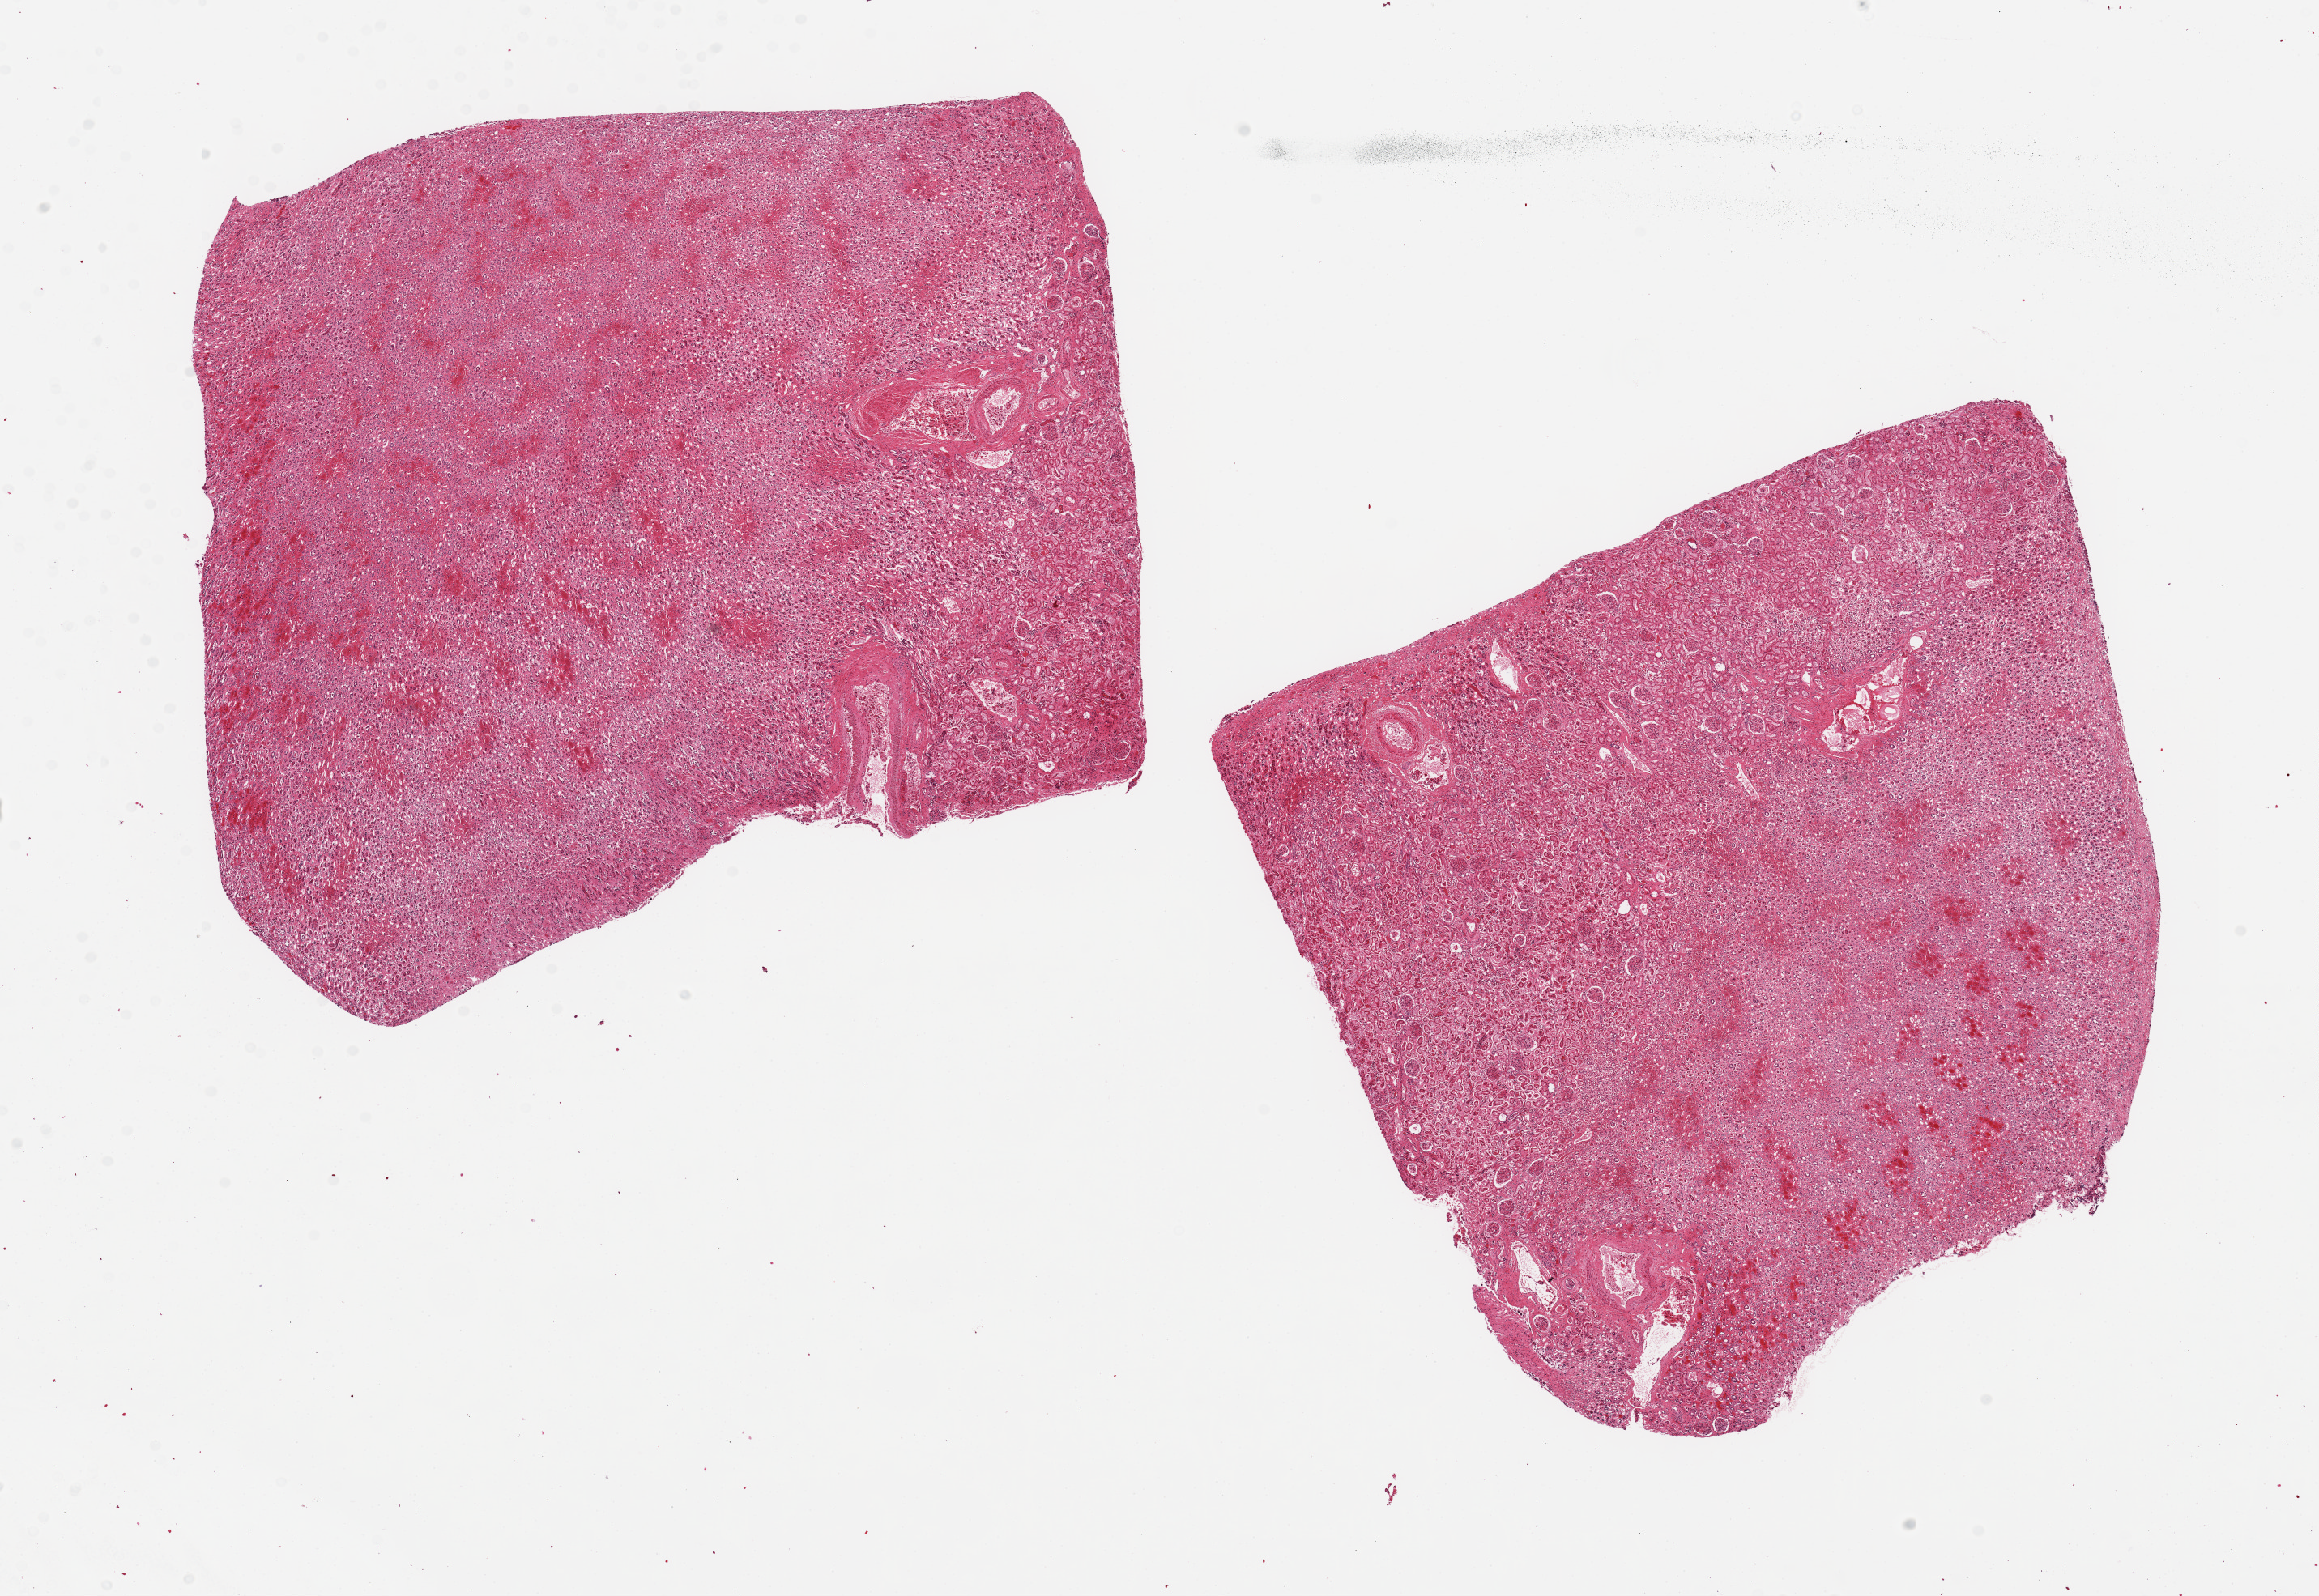
Haematoxylin and eosin whole-slide image, a low-resolution overview of the entire scanned area, about 22.6 x 15.6 mm (acquisition: 20x scan); PAXgene-fixed, paraffin-embedded tissue; section of renal medulla (target tissue); donor tissue sample.
Pathologist's review note for this sample: 2 pieces up to 9x8 mm; one piece has 40% cortex other has 10% cortex; hyperemia and red cell casts.